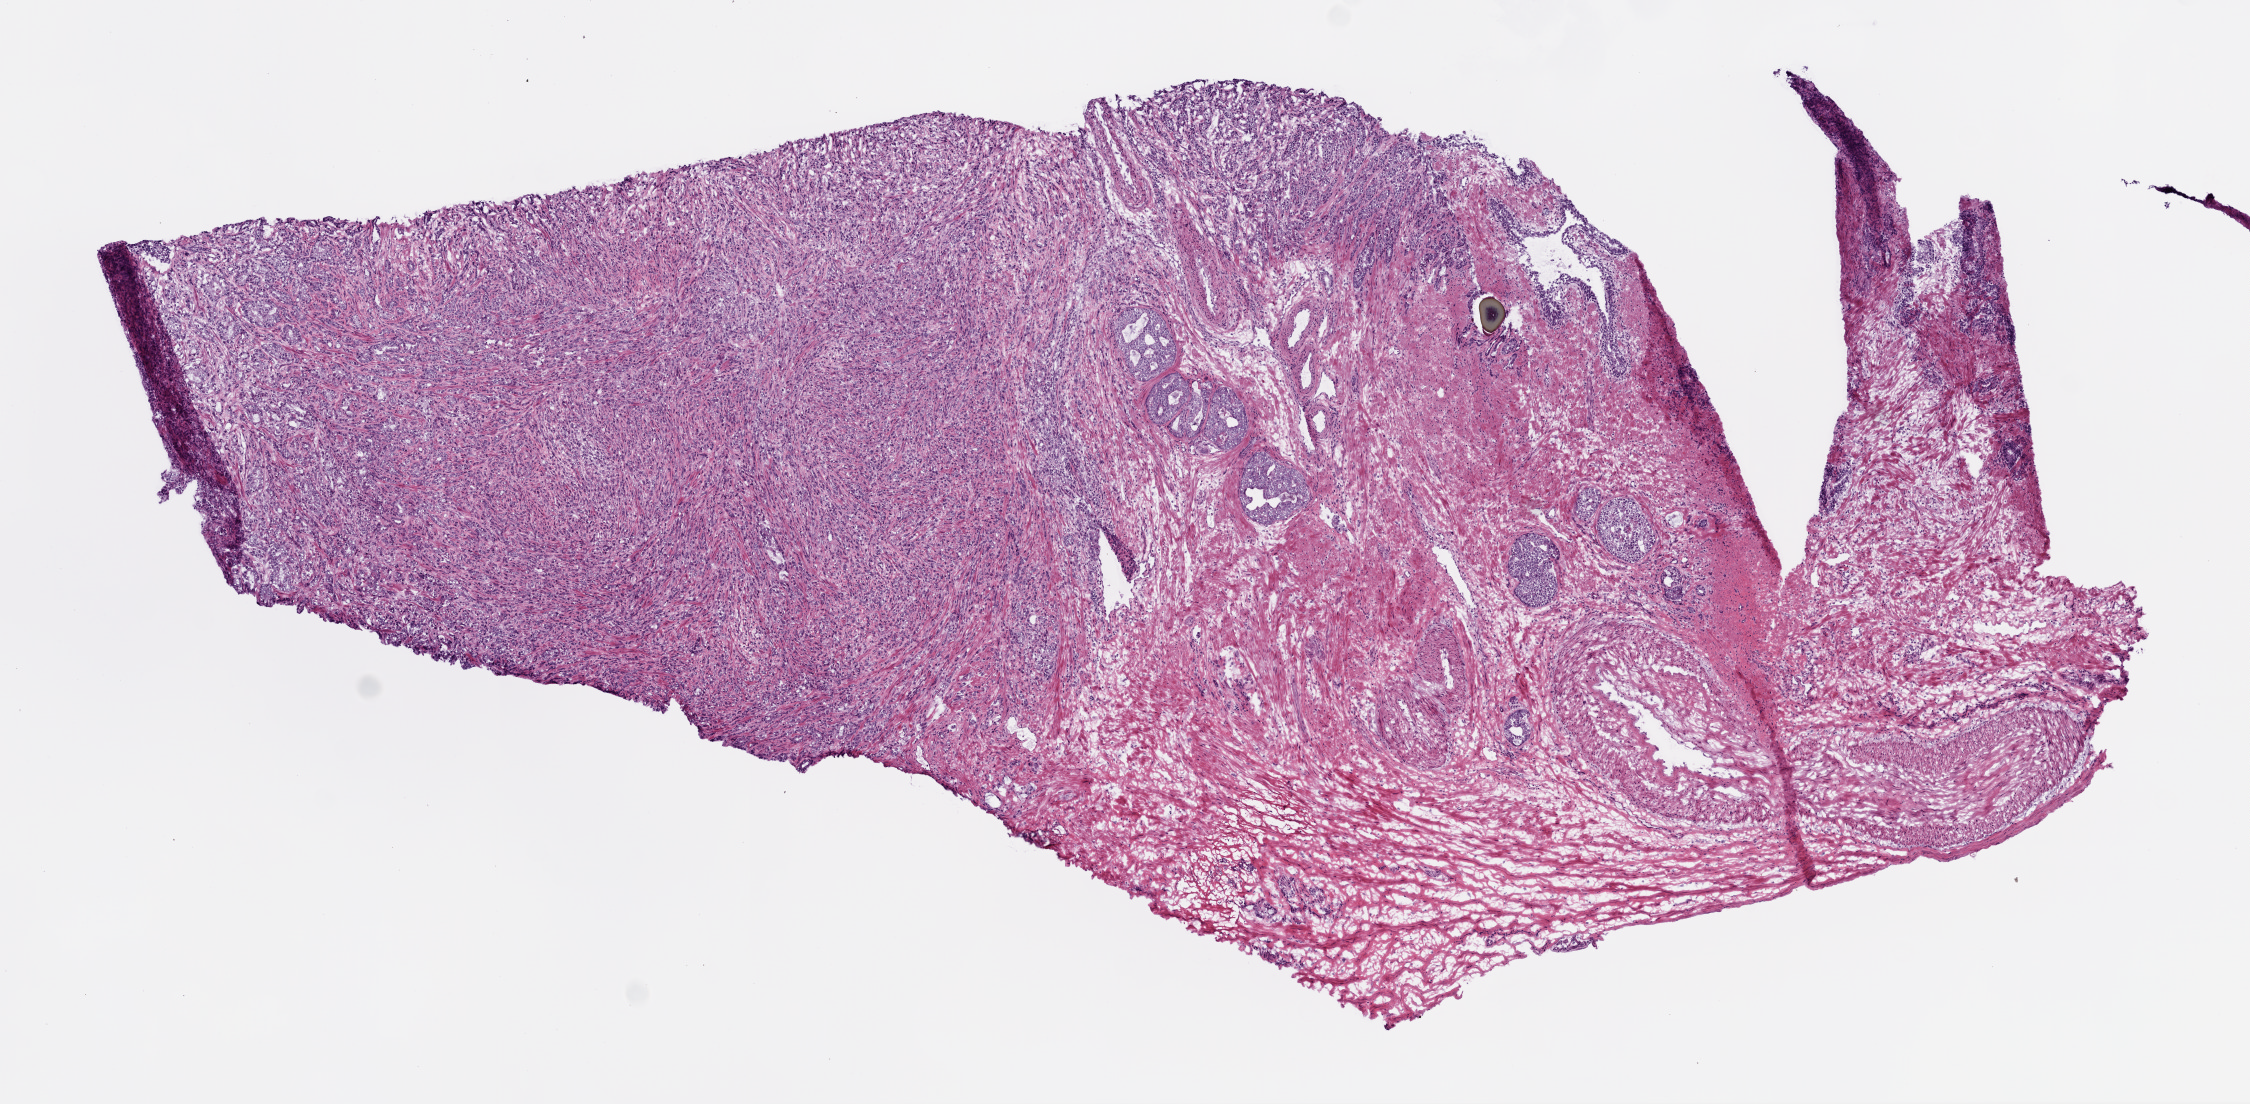
Digitized H&E tissue section (whole slide), a low-resolution overview of the entire scanned area, about 9.0 x 4.4 mm (slide scanned at 20x); frozen section; prostate, primary tumour sample. Patient: male, age at initial diagnosis 63 years. Gleason score: 7 (4+3). Slide review estimates, as recorded: tumour cells 85%, tumour nuclei 80%, normal cells 5%, stromal cells 15%, necrosis 0%. Inflammatory infiltration, as recorded: lymphocyte infiltration 2%, monocyte infiltration 0%, neutrophil infiltration 0%.
Lymph nodes positive (case pathology): 0 of 2 examined. Pathologic diagnosis: Acinar cell carcinoma (prostate gland). Laterality: bilateral.